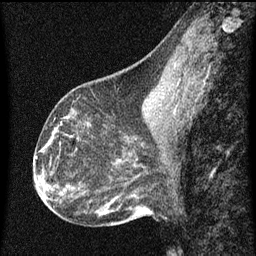
Breast MRI (dynamic contrast-enhanced), one sagittal slice. Slice 29 of 60 in the series (ordered by position). Dynamic contrast-enhanced series, image 2 of 3 at this slice position (ordered by acquisition). 1.5 T. TE 4.2 ms, TR 8 ms. 2 mm slice thickness. 256 × 256 image matrix, field of view 180 × 180 mm. Patient: female, 43 years.
Outlined on this slice (semi-automatically segmented with operator editing):
- analysis volume of interest (the breast-tissue region the enhancement analysis was run in; not a lesion): bounding box <53,104,101,151> (left, top, right, bottom; pixels)
- tumour enhancement mask (voxels above the 70 % enhancement threshold inside the analysis volume of interest): <60,118,71,137>